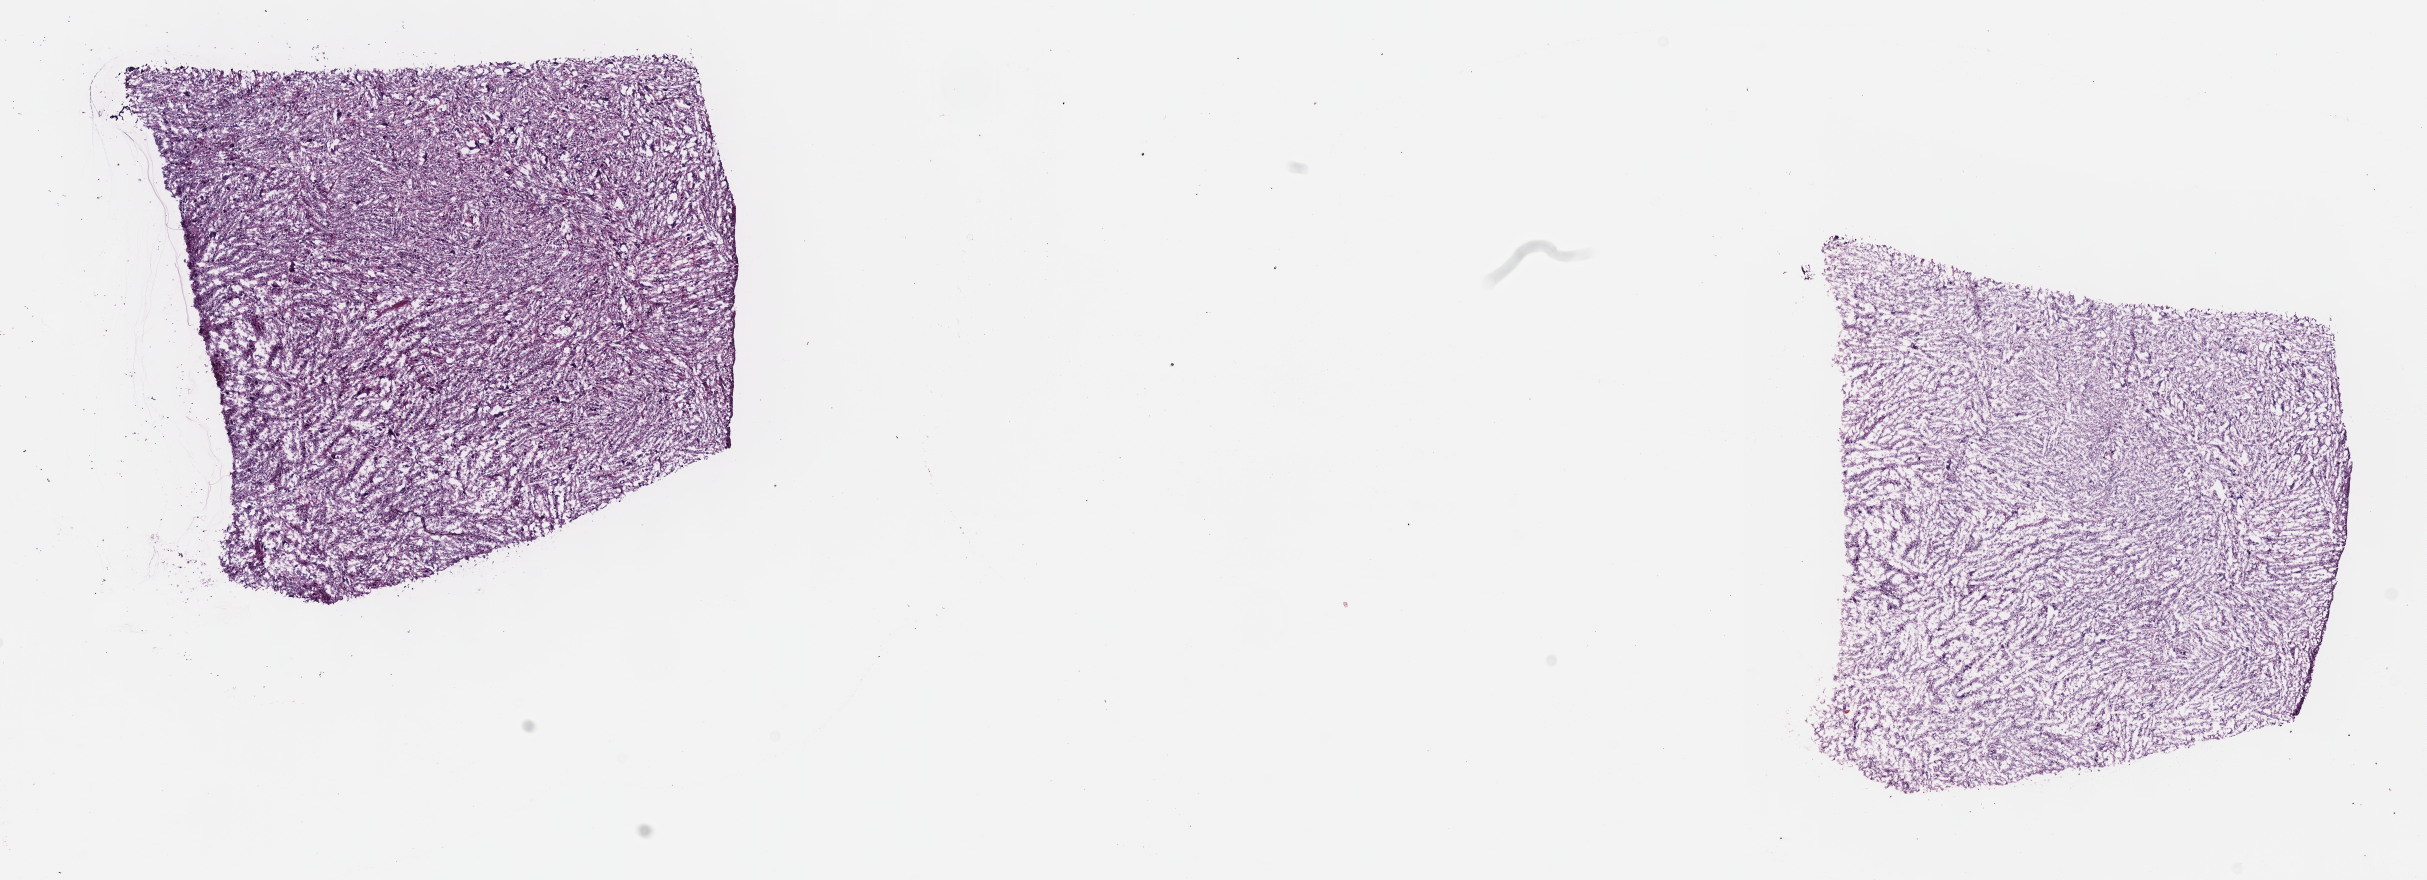
Whole-slide histology image, H&E-stained — whole scanned area (about 19.6 x 7.1 mm, acquisition: 40x scan) shown as a low-resolution overview. Frozen section from the top of the tissue portion. Primary tumour sample from the connective, subcutaneous and other soft tissues. Patient: male, age at initial diagnosis 71 years. Pathologist review of this section (percent, as recorded): tumour cells 100%, tumour nuclei 95%, normal cells 0%, stromal cells 0%, necrosis 0%. Infiltration values recorded for this section: lymphocyte infiltration 0%, monocyte infiltration 0%, neutrophil infiltration 0%.
Diagnosis: Undifferentiated sarcoma (connective, subcutaneous and other soft tissues of trunk, NOS).